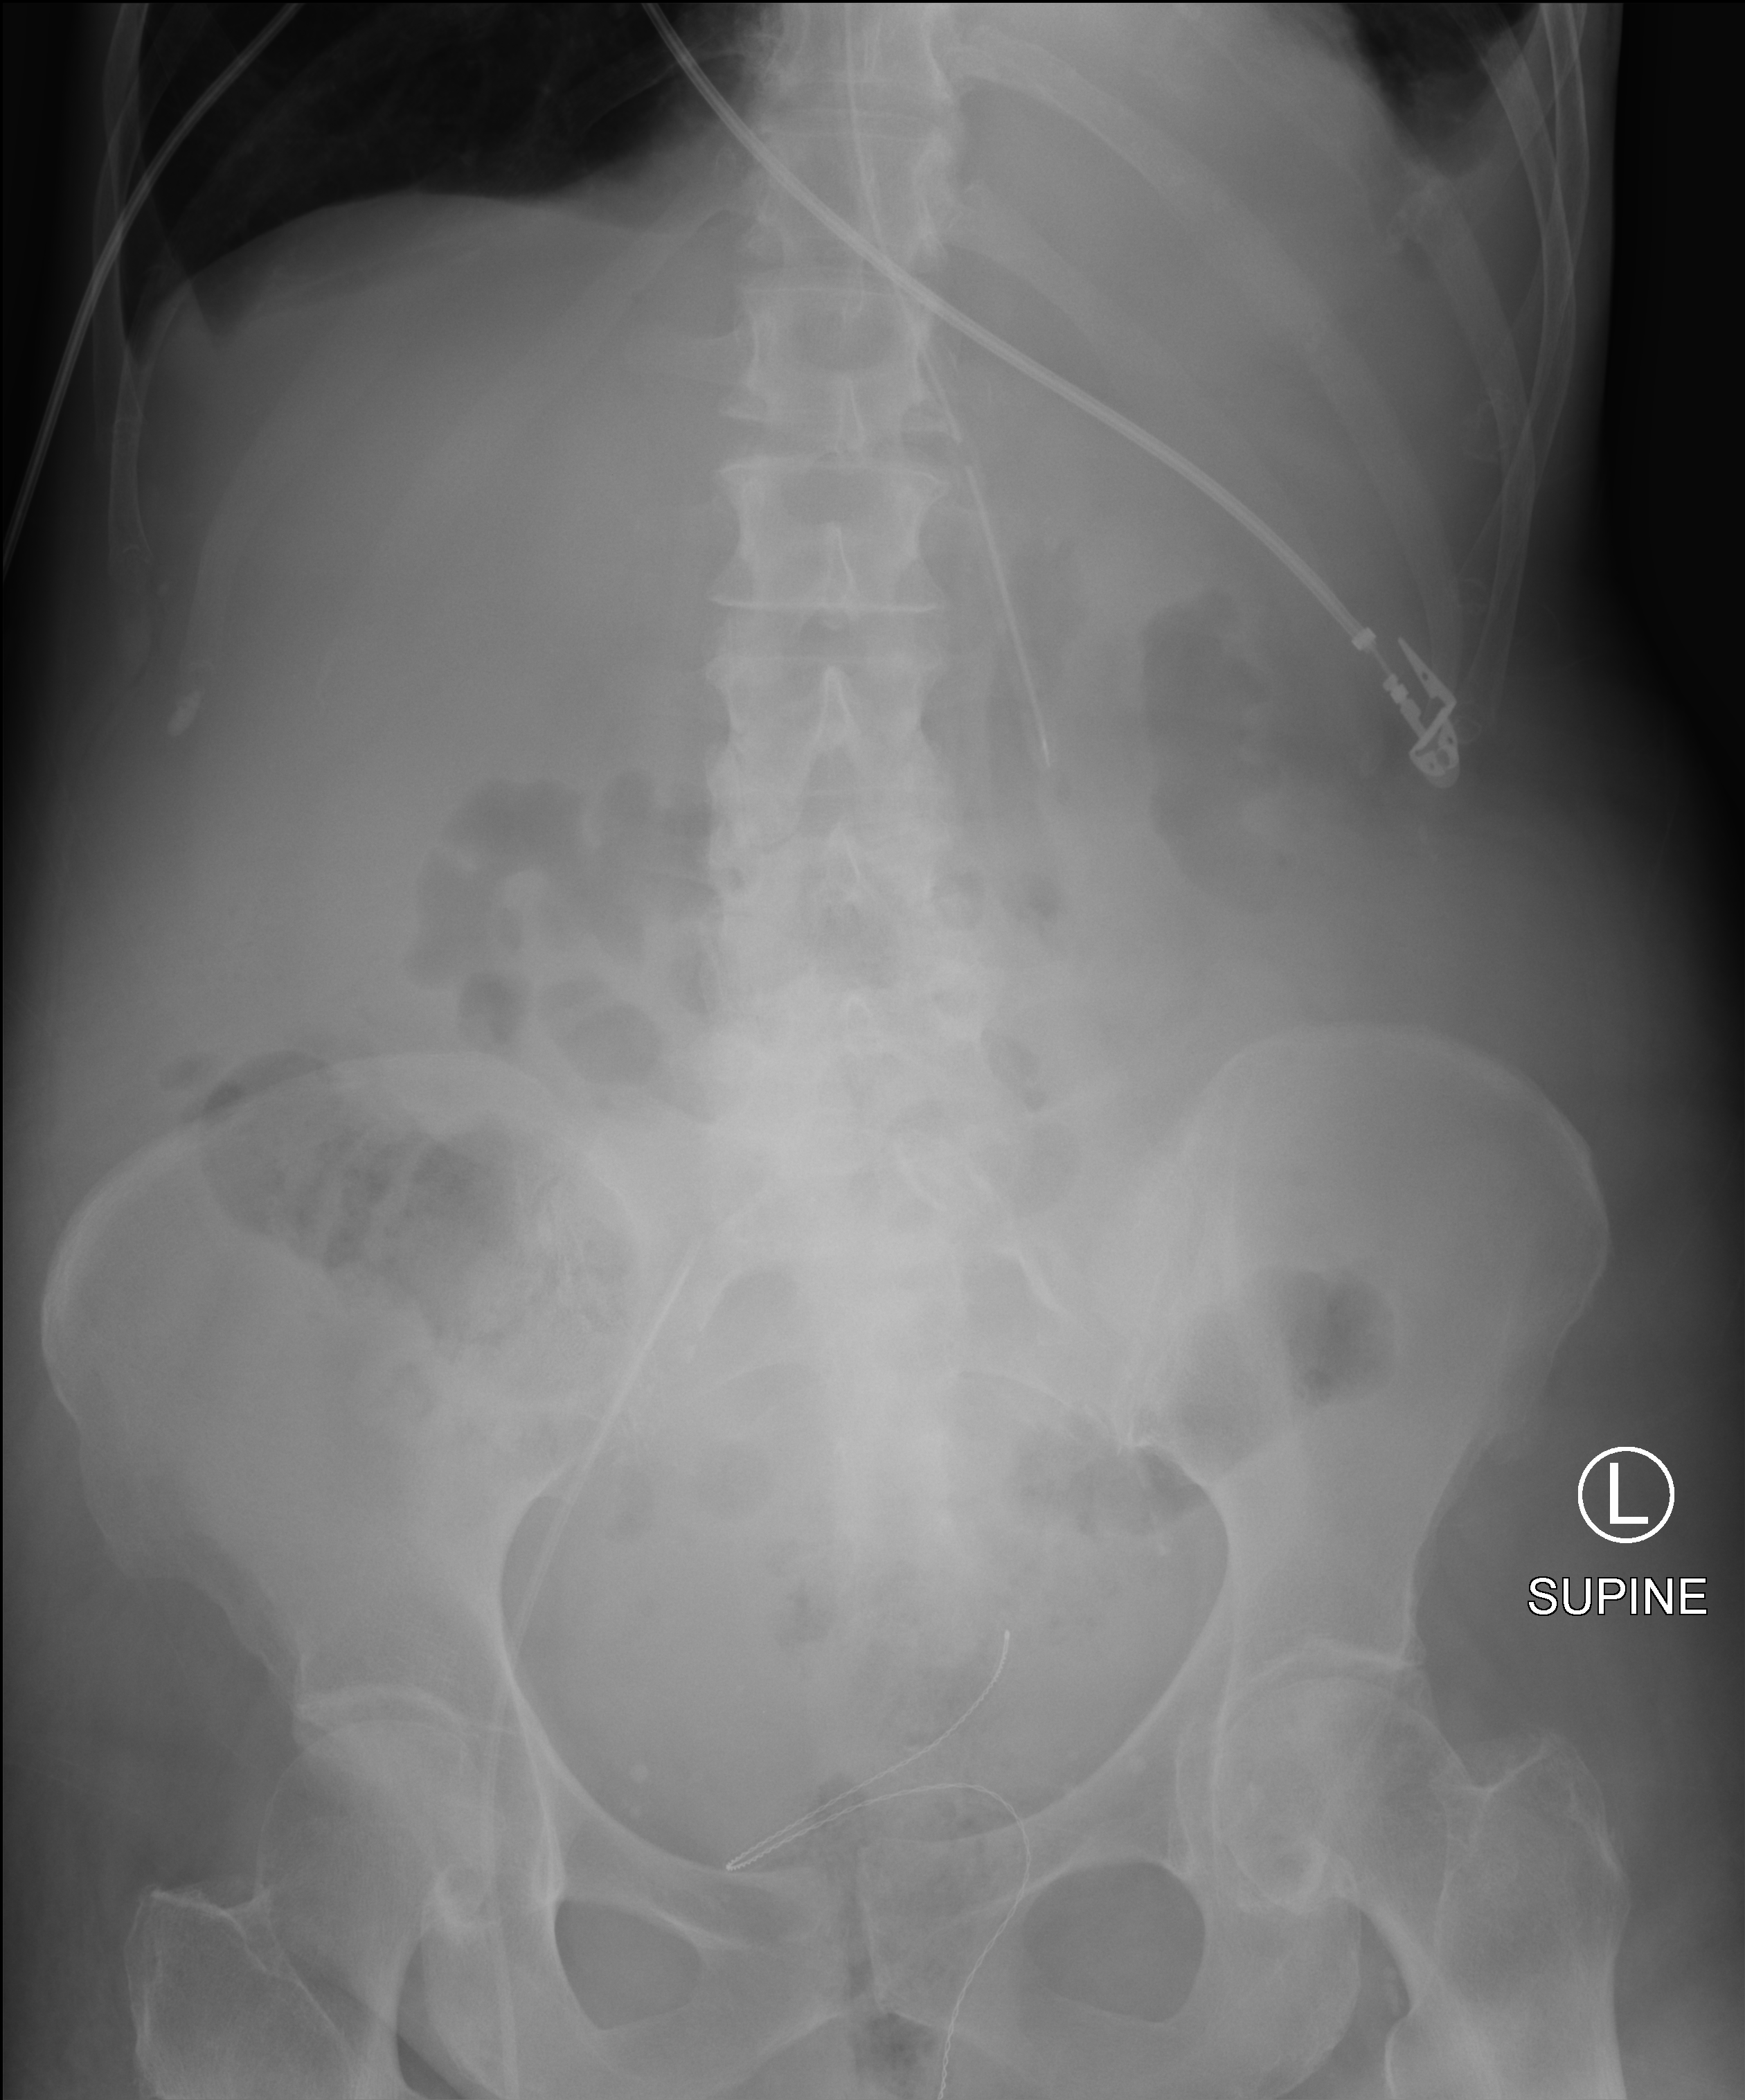
Abdomen X-ray (portable), anteroposterior (AP) projection. Female patient hospitalised with COVID-19, age 60–74 years.
Hospital-stay facts (about this admission, not read from this image; timing relative to this image not recorded):
- length of hospital stay: 38 days
- admitted to intensive care during this hospital stay: yes